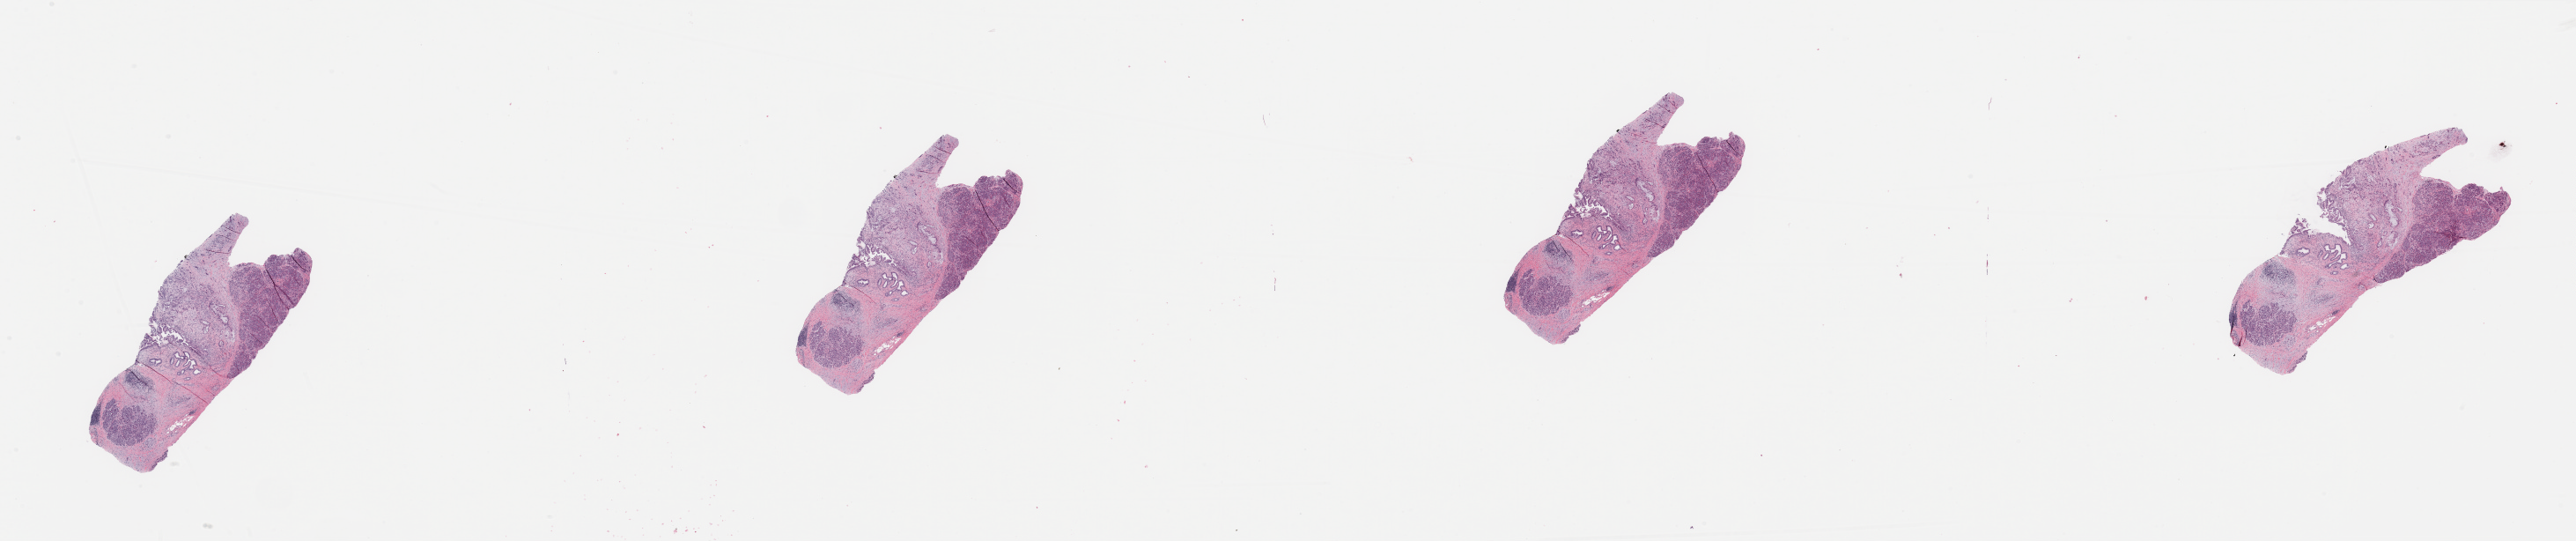
H&E whole-slide image — whole scanned area (about 46.3 x 9.7 mm, slide scanned at 20x) shown as a low-resolution overview. Tumour tissue sample, sampled site: pancreas. Patient: female, age 69 years.
Histologic diagnosis: Infiltrating duct carcinoma, NOS.